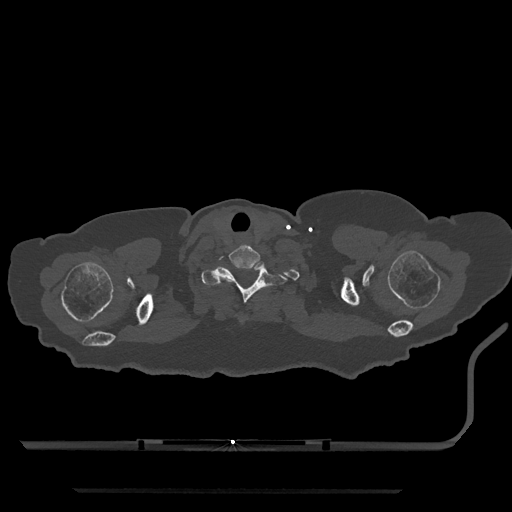
CT including the spine, one axial slice; slice 720 of 797 in the series (ordered by position); reconstruction kernel Br40s/3; bone window (W 1800 / L 400 HU); 0.5 mm slice thickness; 512 × 512 image matrix, field of view 440 × 440 mm. Female patient, age 51 years. Case-level facts recorded for this patient, not image findings: primary cancer: neuro; vertebrae with lytic lesions (as recorded): T8.
Outlined on this slice (semi-automatic segmentation, software-assisted and operator-edited):
- T1 vertebra: box from (x=201, y=262) to (x=287, y=303) px